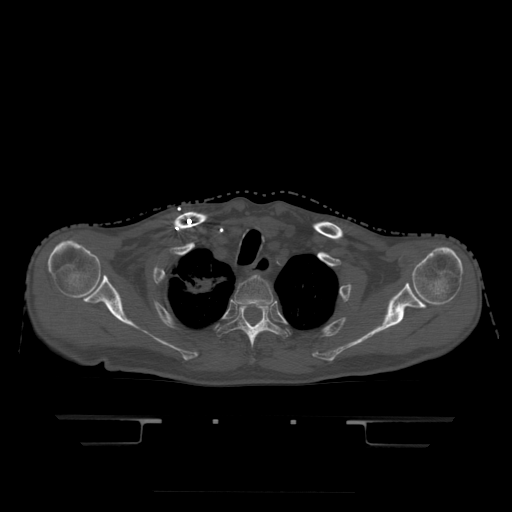
CT including the spine, one axial slice. Bone window (W 1800 / L 400 HU). 1.25 mm slice thickness. 512 × 512 image matrix. Patient age 68 years. From the clinical record (not read from this slice): primary cancer: urothelial.
Outlined on this slice (semi-automatically segmented with operator editing):
- T2 vertebra: bounding box [x1, y1, x2, y2] px = [234, 277, 274, 304]
- T3 vertebra: [217, 303, 281, 364]